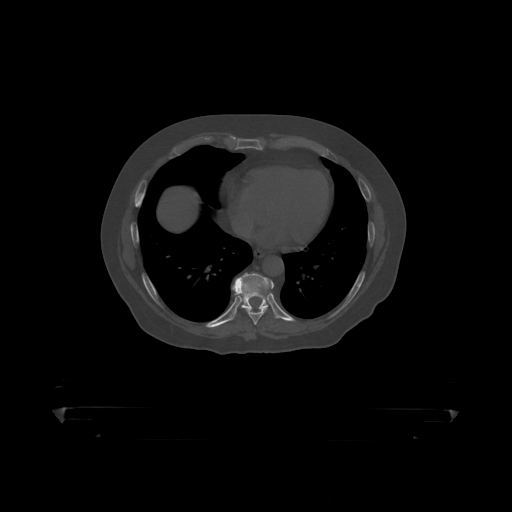
CT including the spine, one axial slice; slice 248 of 390 in the series (ordered by position); reconstruction kernel STANDARD; 120 kVp; bone window (W 1800 / L 400 HU); 512 × 512 image matrix, field of view 650 × 650 mm. Patient: male, 60 years. From the clinical record (not read from this slice): primary cancer: prostate.
Structures marked on this image (semi-automatic segmentation, software-assisted and operator-edited):
- T8 vertebra: bounding box <247,281,275,319> (left, top, right, bottom; pixels)
- T9 vertebra: <232,273,270,315>